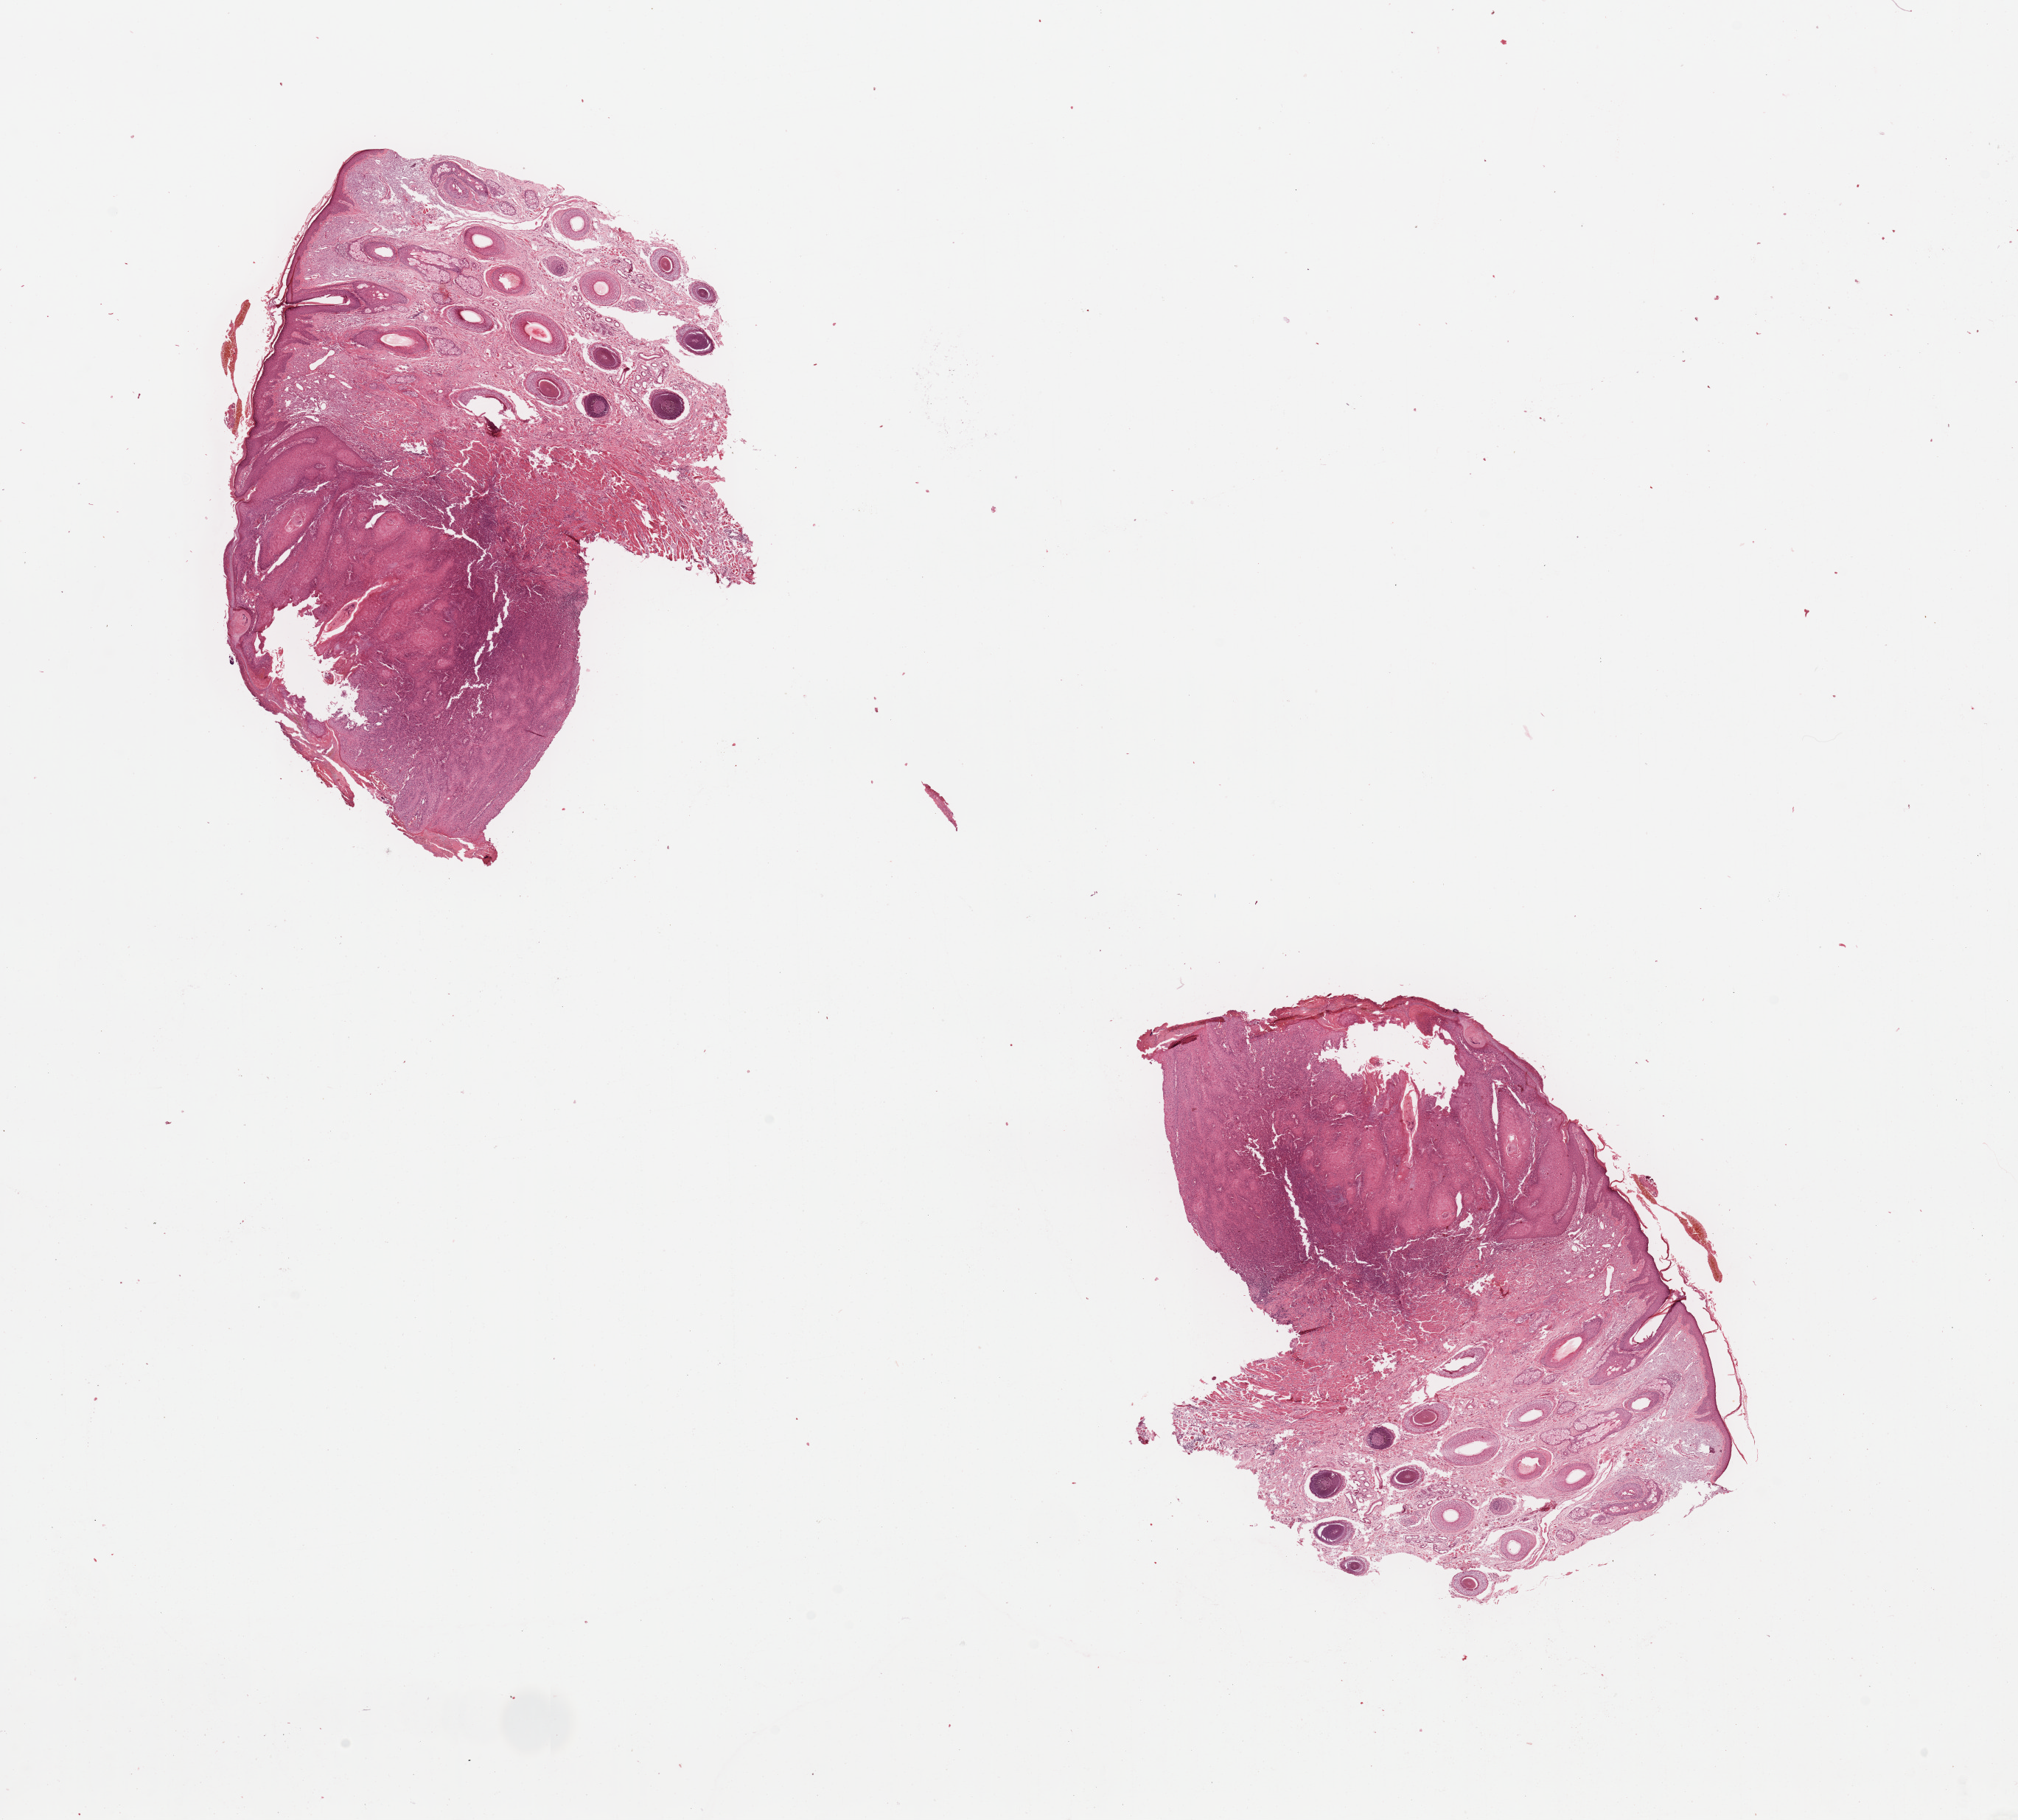
Whole-slide histology image, H&E, a low-resolution overview of the entire scanned area, about 21.7 x 19.5 mm. Head and neck, tissue type not recorded. Patient: male, age 76 years.
Patient diagnosis: Squamous cell carcinoma, NOS (lip, NOS).